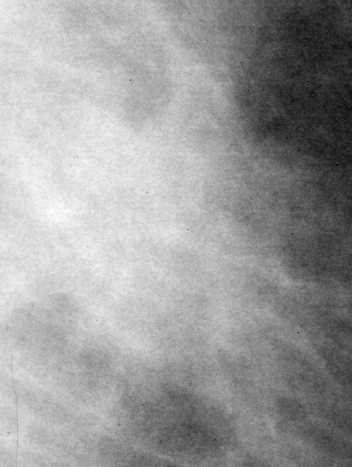
Cropped region of a digitized screen-film mammogram centred on a radiologist-marked abnormality, left breast, MLO view.
- Mass, shape irregular, margins spiculated; BI-RADS assessment category 4; subtlety rating 4 on a 1 (subtle) to 5 (obvious) scale; pathology (as recorded): malignant.